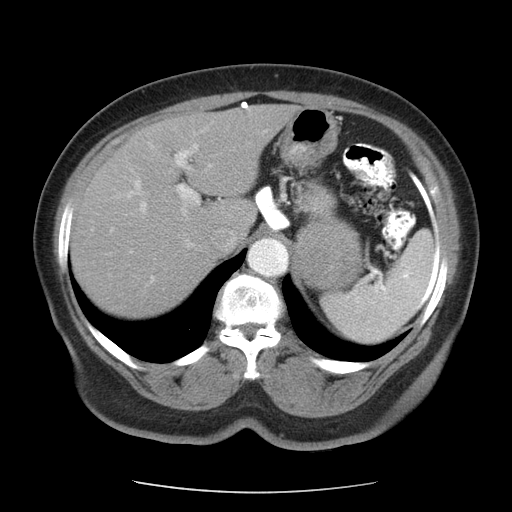
Contrast-enhanced abdominal CT, one axial slice; reconstruction kernel STANDARD; intravenous contrast given; soft-tissue window (W 400 / L 40 HU); 5 mm slice thickness; 512 × 512 image matrix, field of view 362 × 362 mm. Patient: female, 71 years. From the clinical record (not read from this slice): diagnosis: adrenocortical carcinoma; tumour side: left adrenal; tumour size at pathology: 8.8 cm; Ki-67 index: 20 %; stage (as recorded): 2.
Outlined on this slice (semi-automatically segmented with operator editing):
- mass: bounding box <296,220,361,289> (left, top, right, bottom; pixels)